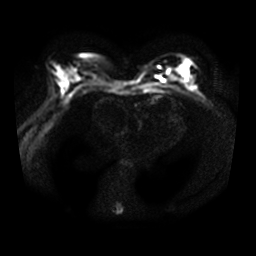
Breast MRI, one axial slice; position 18 of 34 along the scan axis; diffusion-weighted series; image 2 of 4 stored at this slice position (different b-values; order by instance number); 3 T; 5 mm slice thickness; 256 × 256 image matrix, field of view 340 × 340 mm. Female patient.
Structures marked on this image (outlined manually by an expert reader):
- tumour on diffusion-weighted imaging: bounding box [x1, y1, x2, y2] px = [181, 66, 189, 75]